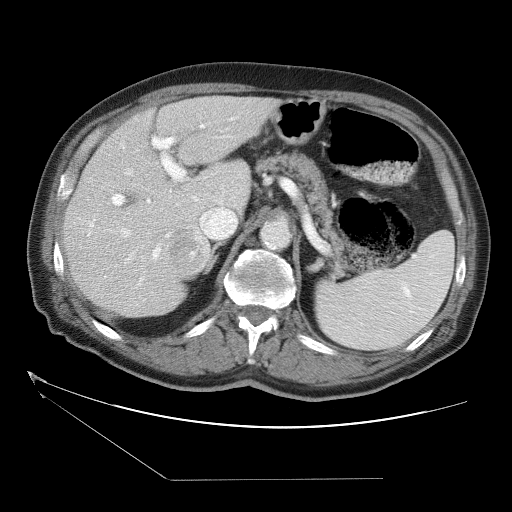
Contrast-enhanced abdominal CT (liver protocol), one axial slice. Reconstruction kernel STANDARD. 120 kVp. One of 2 acquisitions stored at this slice position. Soft-tissue window (W 400 / L 40 HU). 5 mm slice thickness. 512 × 512 image matrix, field of view 400 × 400 mm. From the clinical record (not read from this slice): diagnosis: hepatocellular carcinoma (patient treated with transarterial chemoembolisation; whether this scan precedes or follows treatment is not stated here); TNM stage (as recorded): Stage-II; Child-Pugh class: A; tumour differentiation: moderately differentiated; tumour size: 0.8 cm.
Structures marked on this image (semi-automatic segmentation, software-assisted and operator-edited):
- liver parenchyma outside the tumour (the mass and vessels are separate outlines, so this box may not span the whole liver): bounding box [x1, y1, x2, y2] px = [62, 96, 280, 316]
- mass: [169, 225, 211, 279]
- liver vessels: [87, 124, 229, 306]